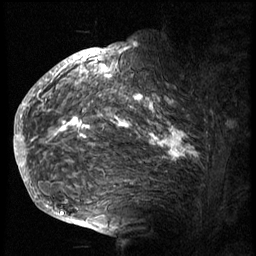
Breast MRI (dynamic contrast-enhanced), one sagittal slice; position 49 of 74 along the scan axis; 3 images stored at this slice position (order not interpretable as contrast timing); 1.5 T; TE 4.2 ms, TR 8.9 ms; 2.5 mm slice thickness; 256 × 256 image matrix. Female patient, age 57 years. From the clinical record (not read from this slice): setting: breast cancer imaged before/during neoadjuvant chemotherapy; receptor status: HER2-positive.
Annotated regions visible in this slice (semi-automatically segmented with operator editing):
- analysis volume of interest (the breast-tissue region the enhancement analysis was run in; not a lesion): bounding box (x1, y1, x2, y2) in pixels: (40, 62, 235, 175)
- tumour enhancement mask (voxels above the 140 % enhancement threshold inside the analysis volume of interest): (47, 63, 193, 161)